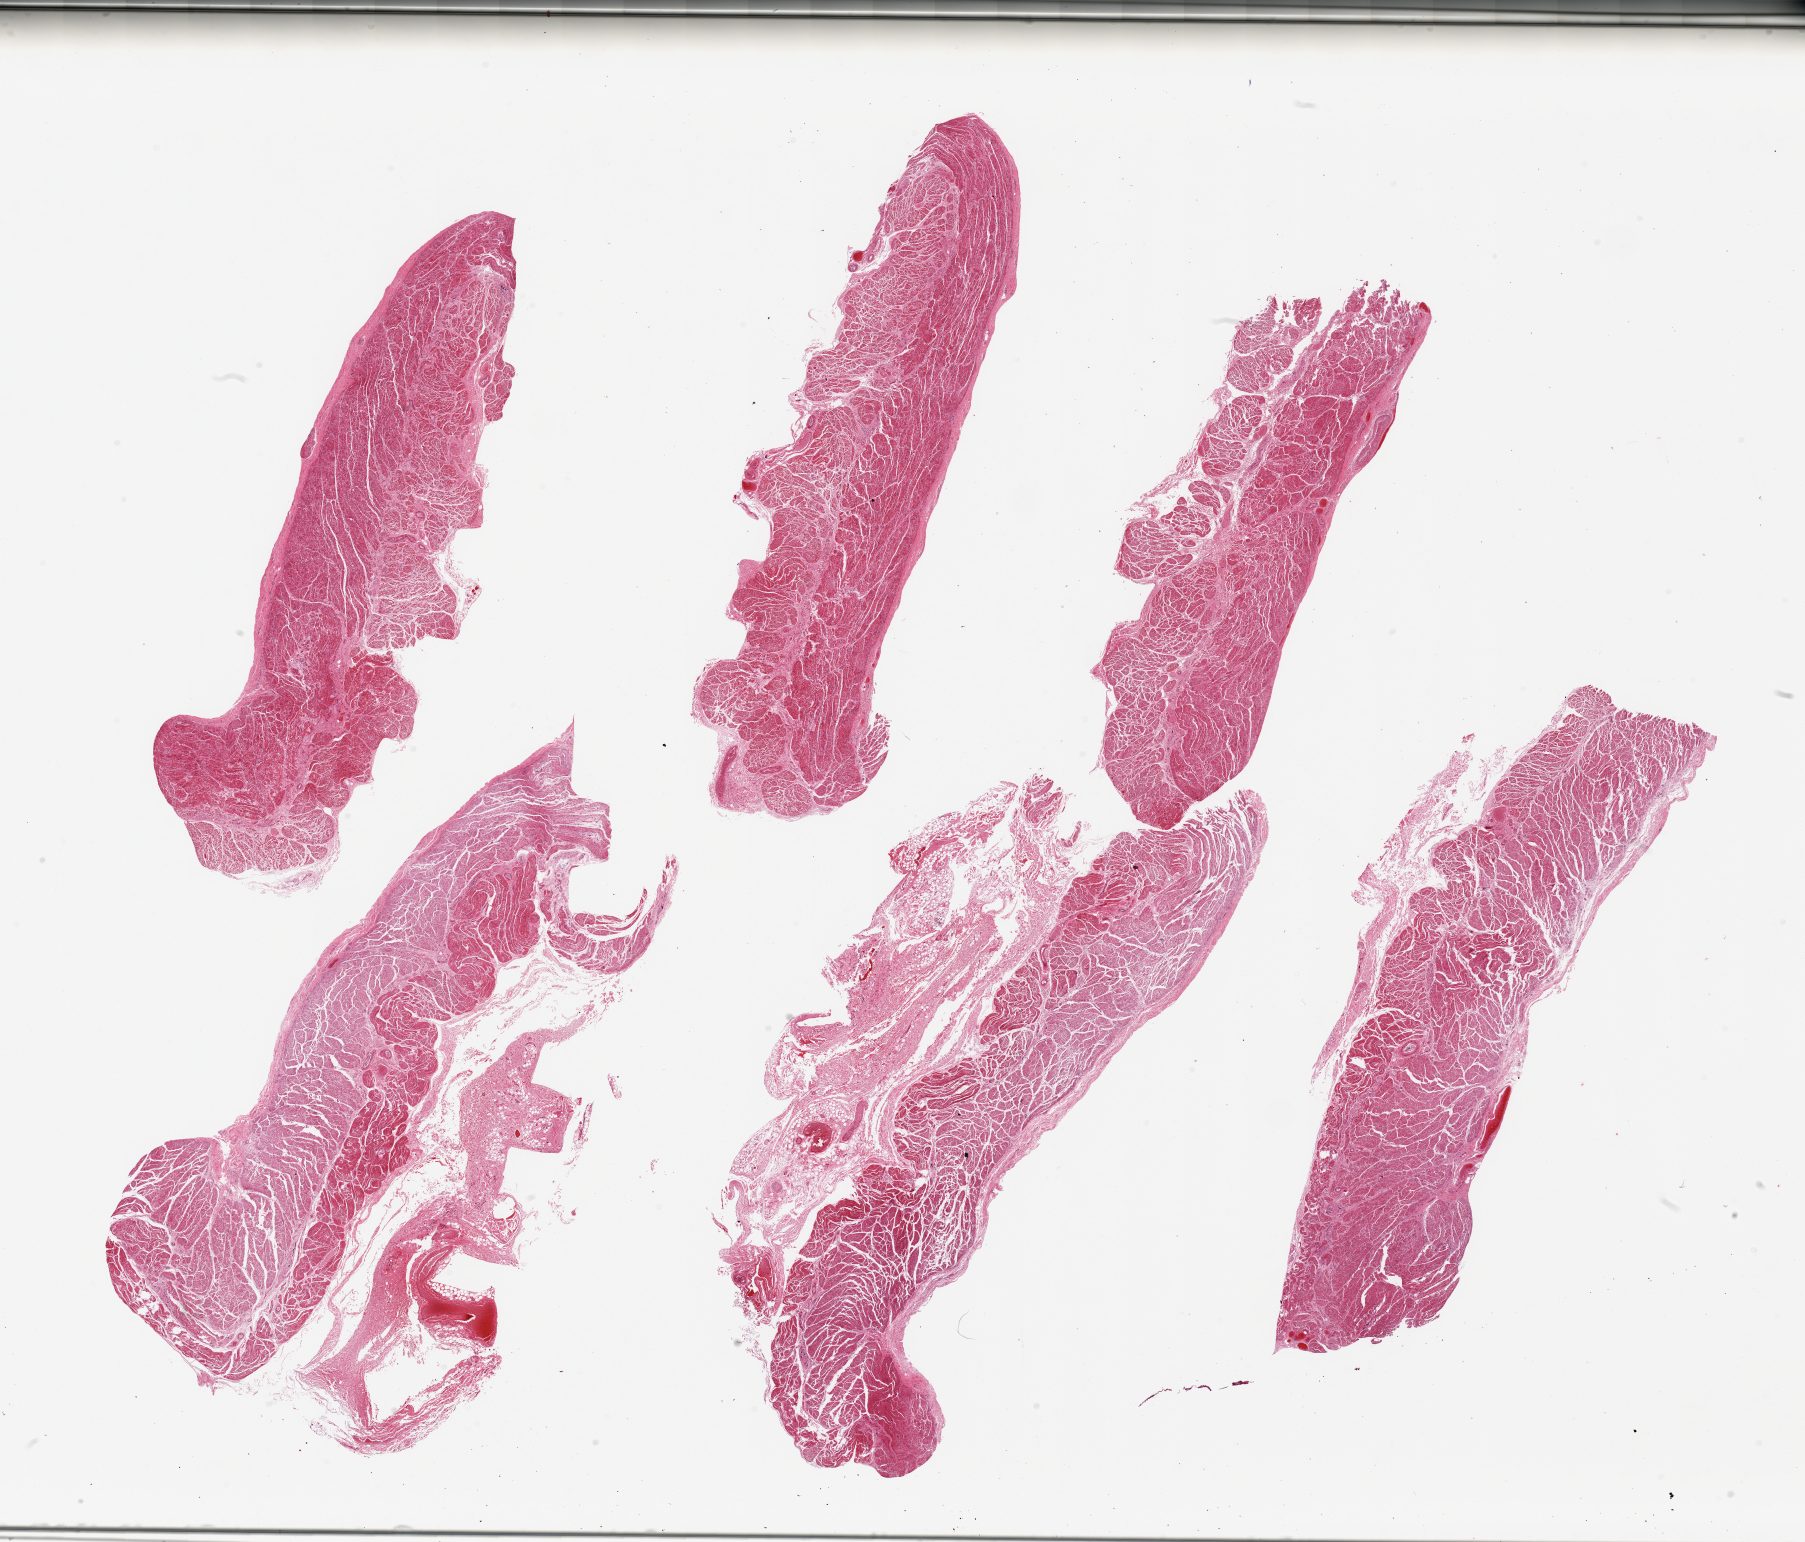
Digitized hematoxylin and eosin (H&E)-stained section, brightfield — low-resolution overview of the scanned area, about 28.5 x 24.4 mm. PAXgene-fixed paraffin-embedded (PFPE) section. Target tissue: esophageal muscle. Donor tissue sample. Donor sex: male.
Pathologist's review note for this sample: 6 pieces; target muscularis with some residual adventitia.